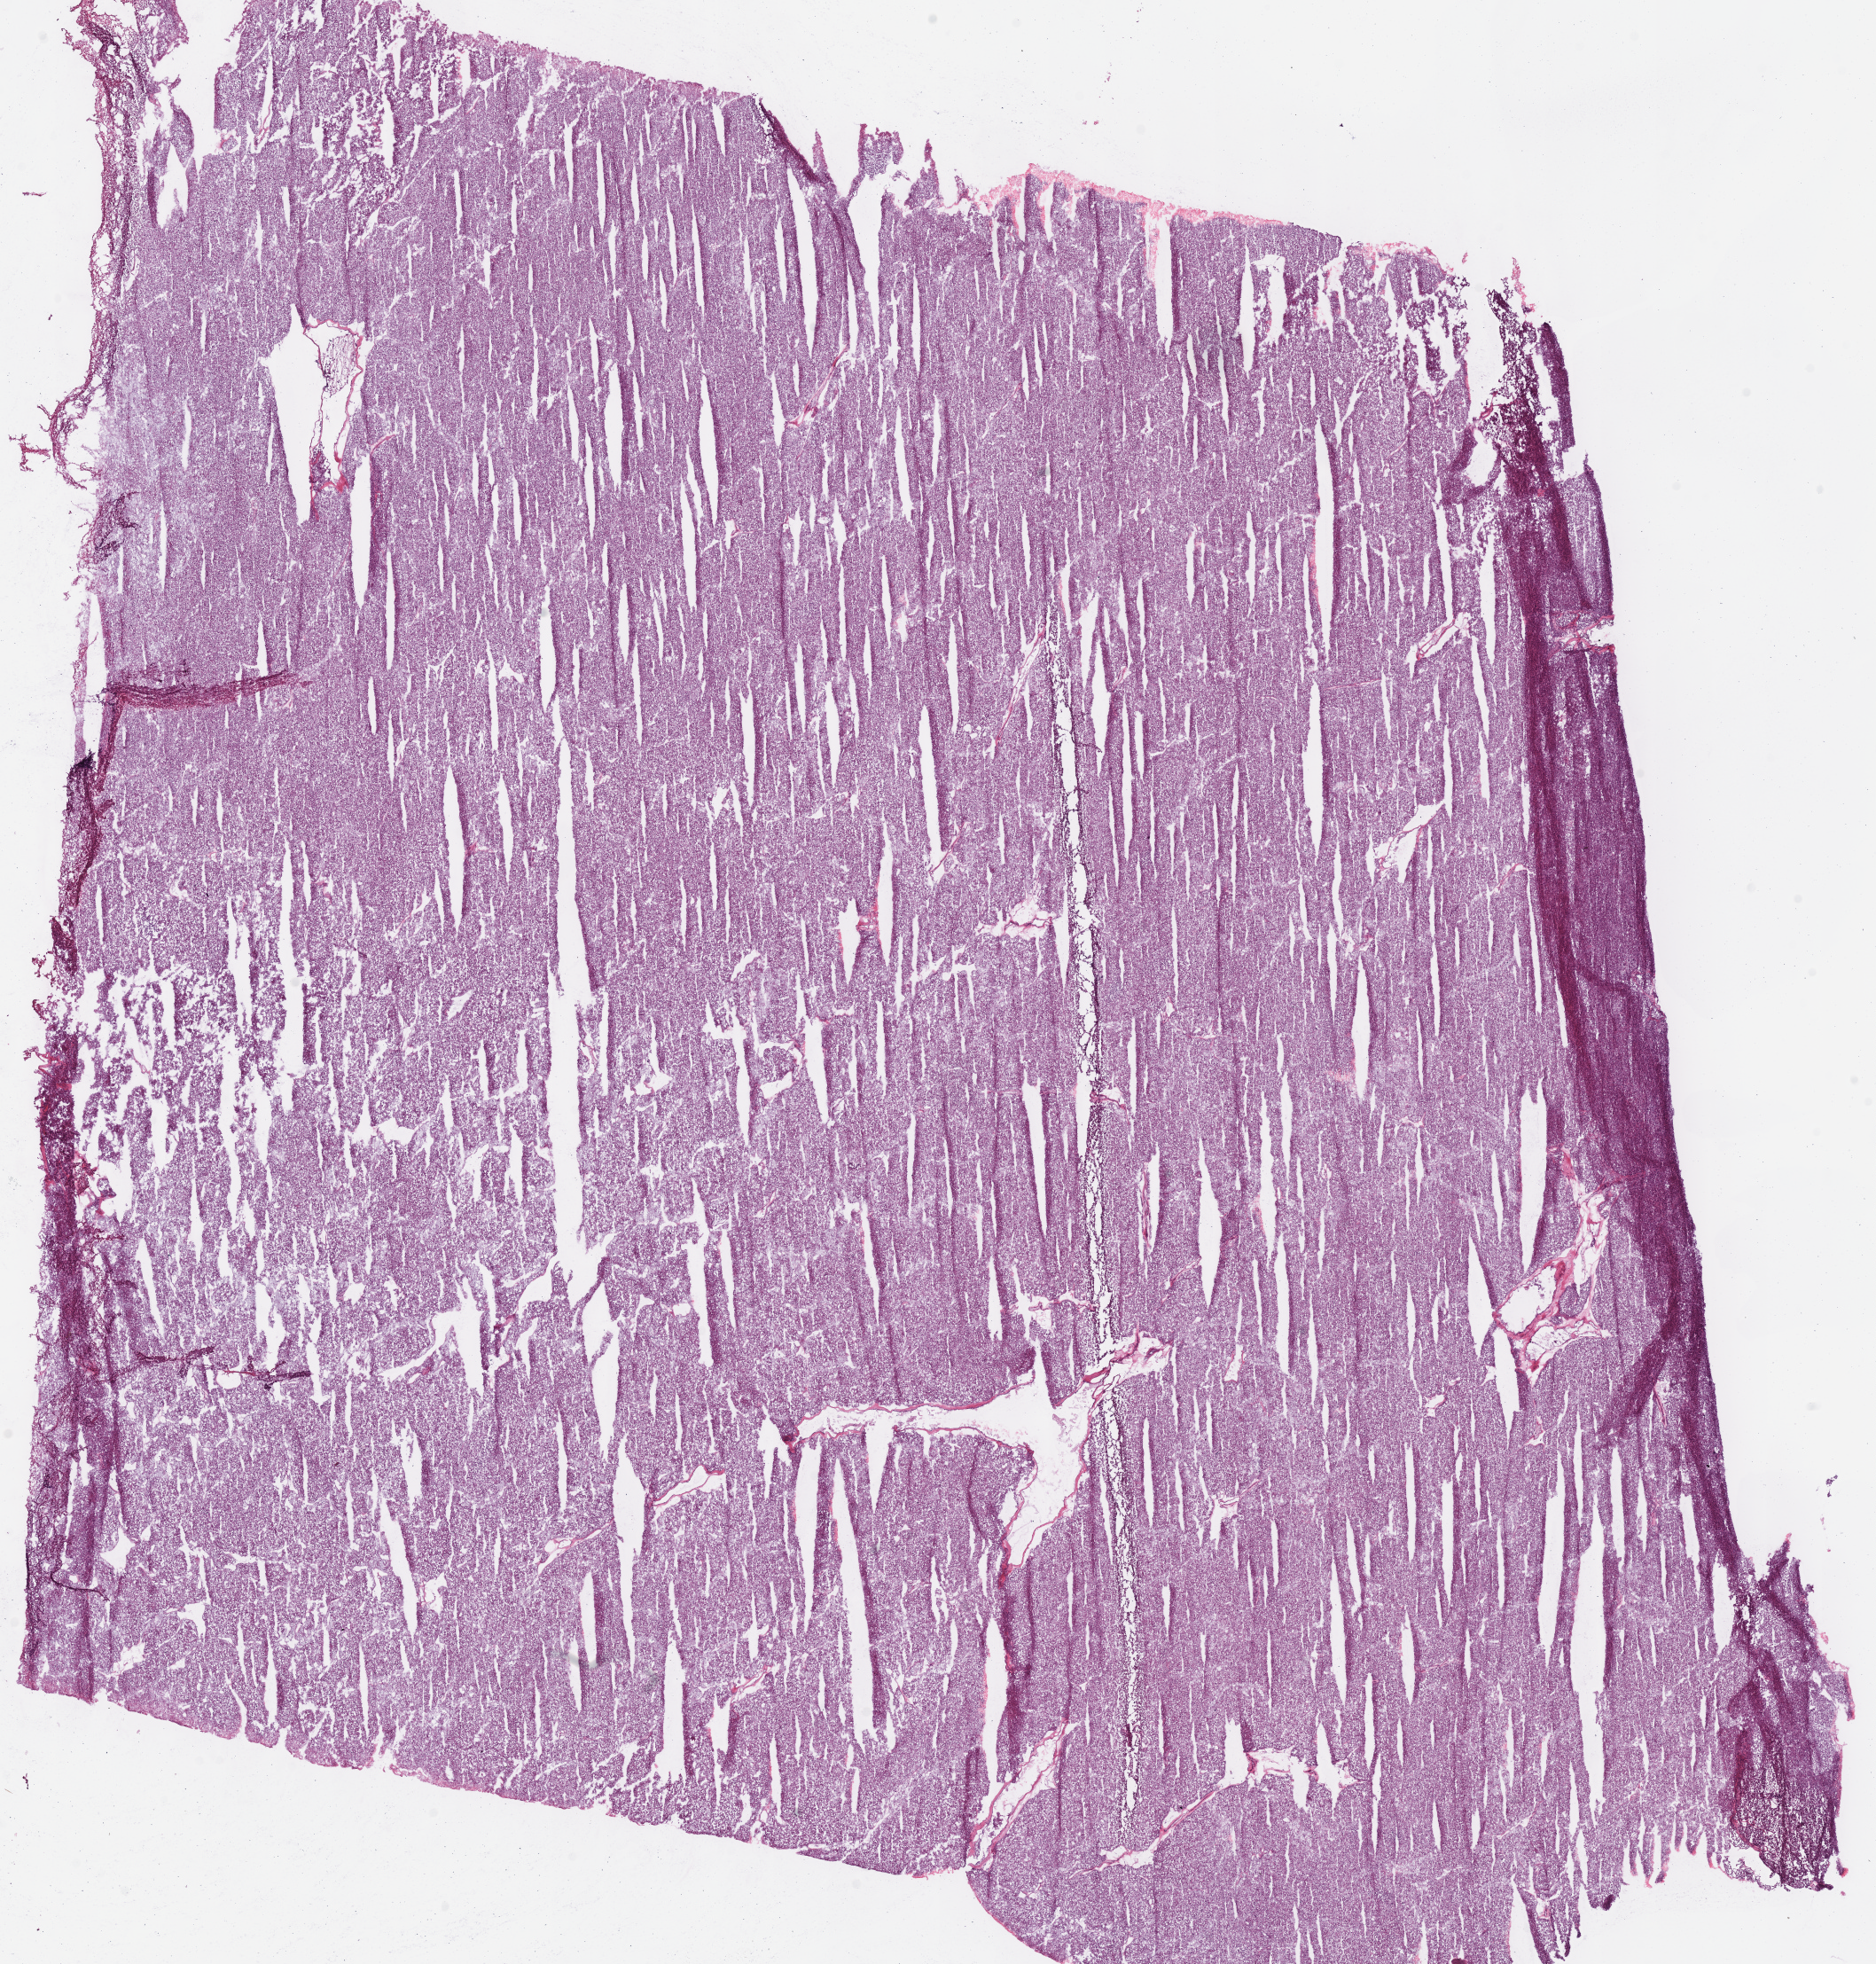
Hematoxylin and eosin (H&E) stained whole-slide image, whole scanned area (about 16.6 x 17.4 mm, acquisition: 40x scan) shown as a low-resolution overview. Frozen section from the bottom of the tissue portion. Sample: primary tumour, kidney. Female patient; age at initial diagnosis 56 years. Pathologist review of this section (percent, as recorded): tumour cells 100%, tumour nuclei 90%.
Diagnosis: Renal cell carcinoma, chromophobe type.